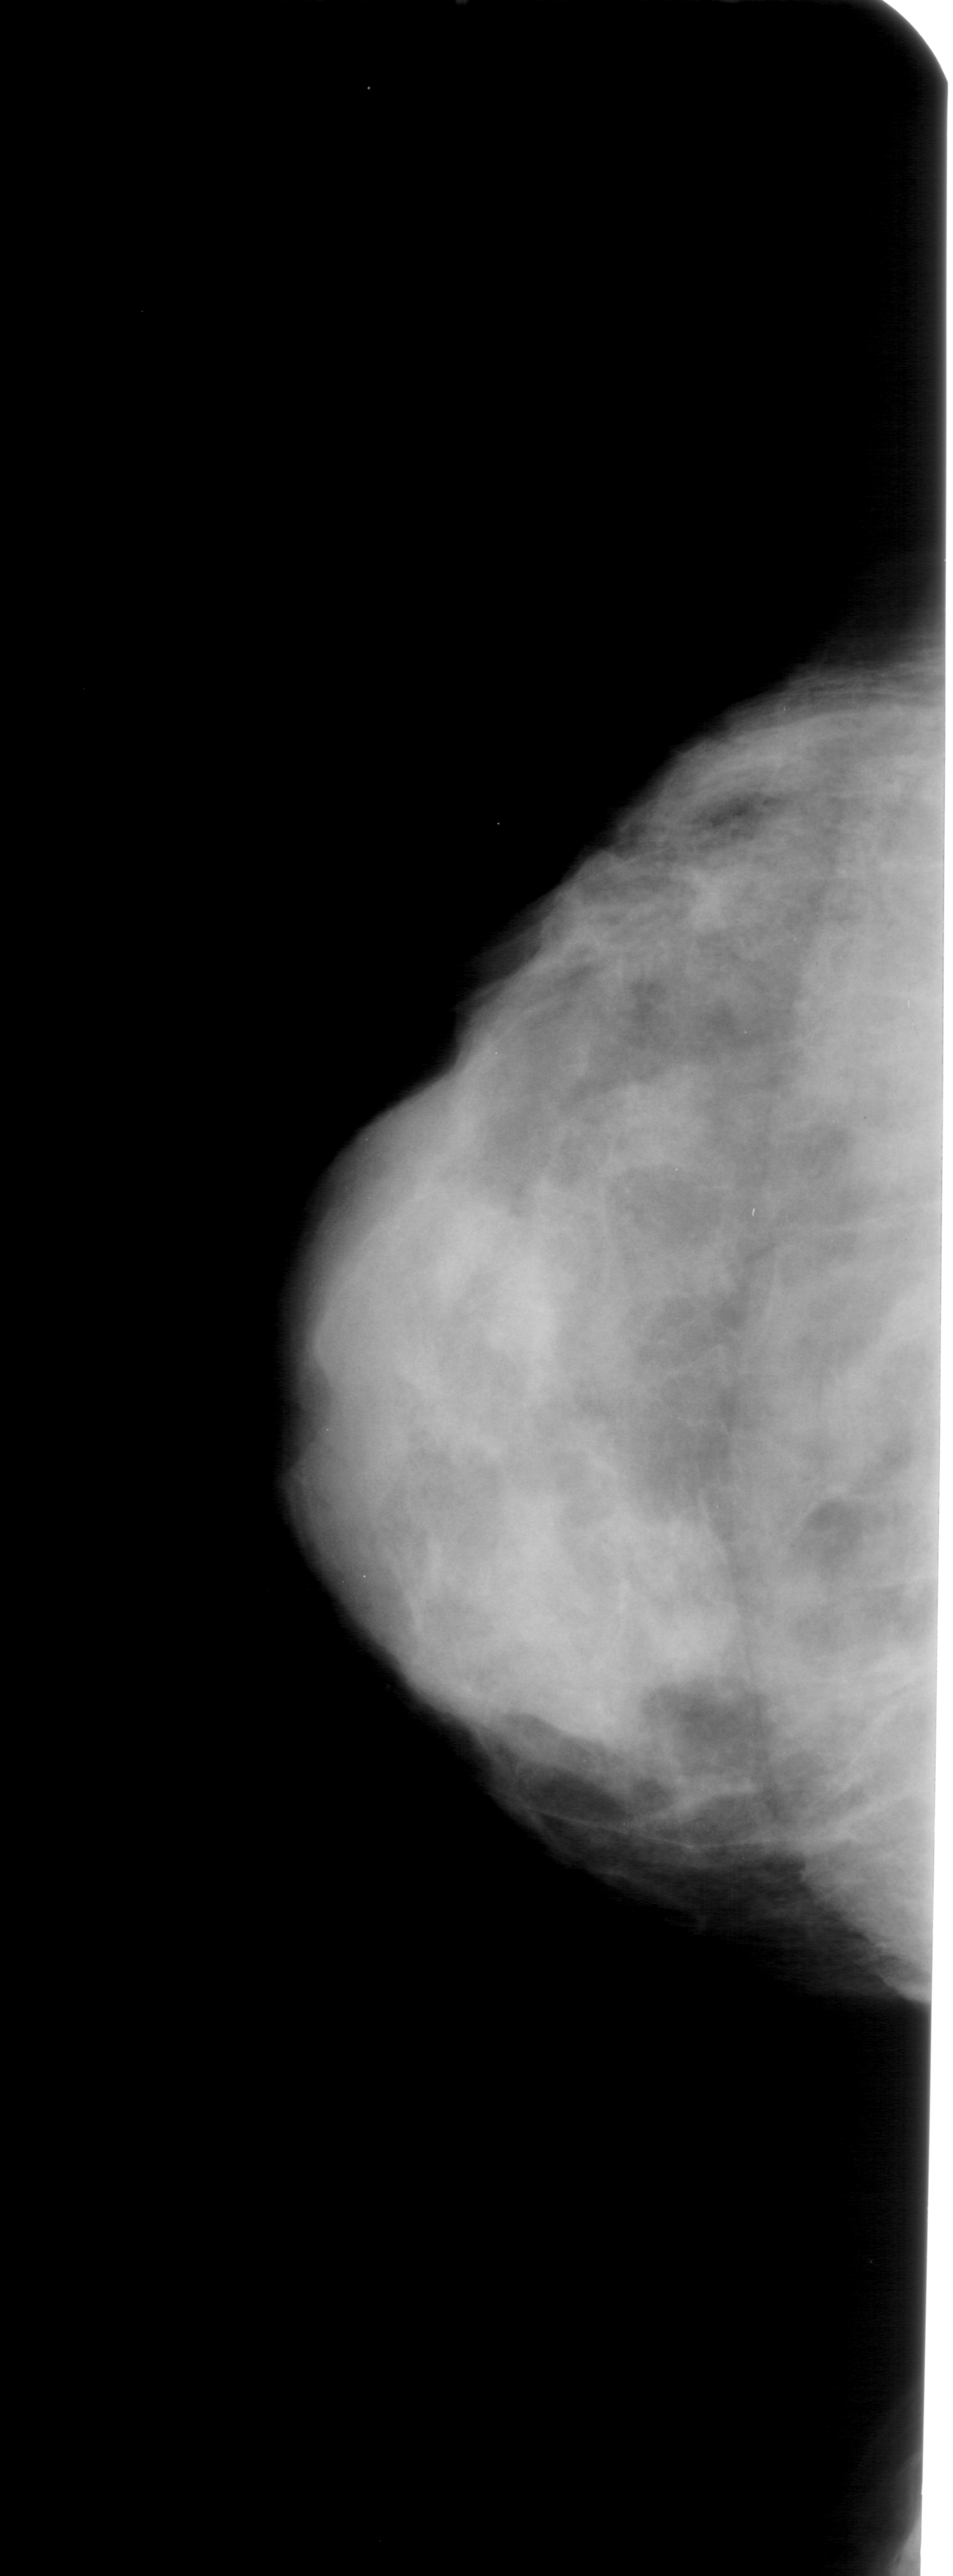
Digitized screen-film mammogram; left breast; craniocaudal (CC) view.
Abnormality record for this image: calcifications, morphology pleomorphic, distribution clustered; BI-RADS assessment category 4; subtlety rating 1 on a 1 (subtle) to 5 (obvious) scale; pathology (as recorded): benign.